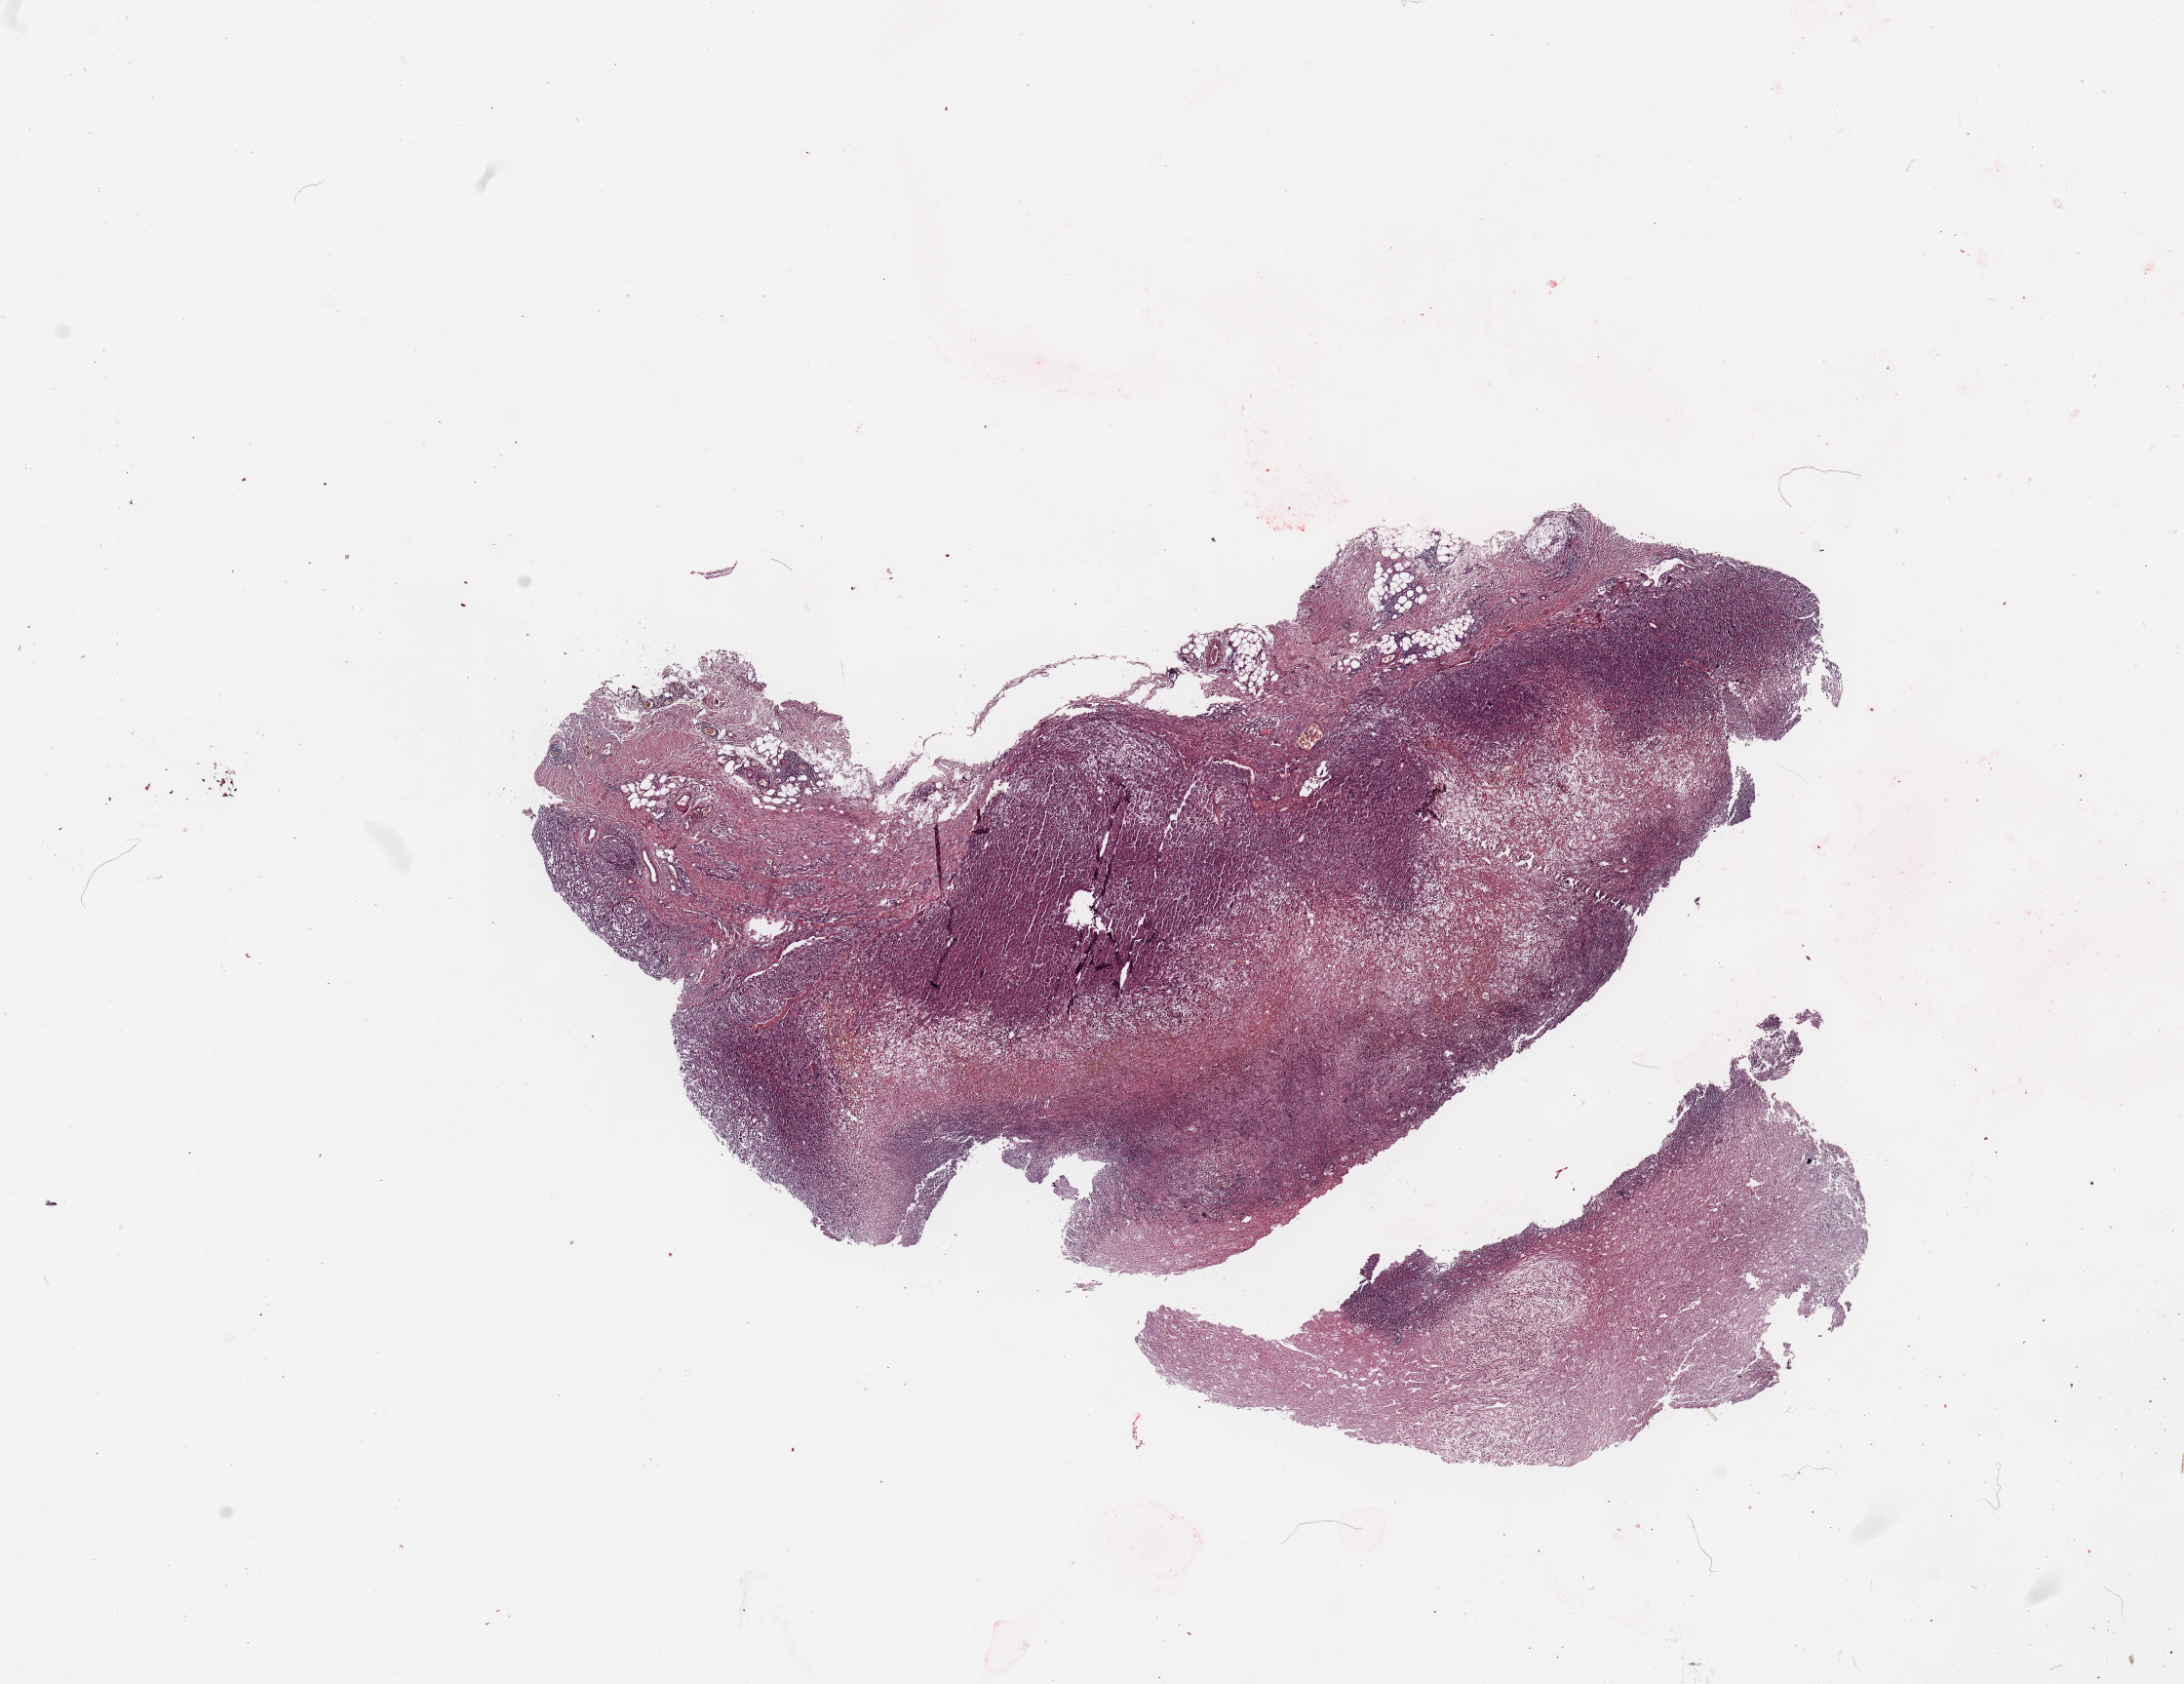
Whole-slide histology image, H&E, low-resolution overview of the scanned area, about 17.7 x 13.7 mm; tumour tissue sample. Patient: male, age 72 years.
Patient diagnosis (cohort enrolment): sarcoma (site not recorded at cohort level). Primary tumour site (as recorded): upper extremity.